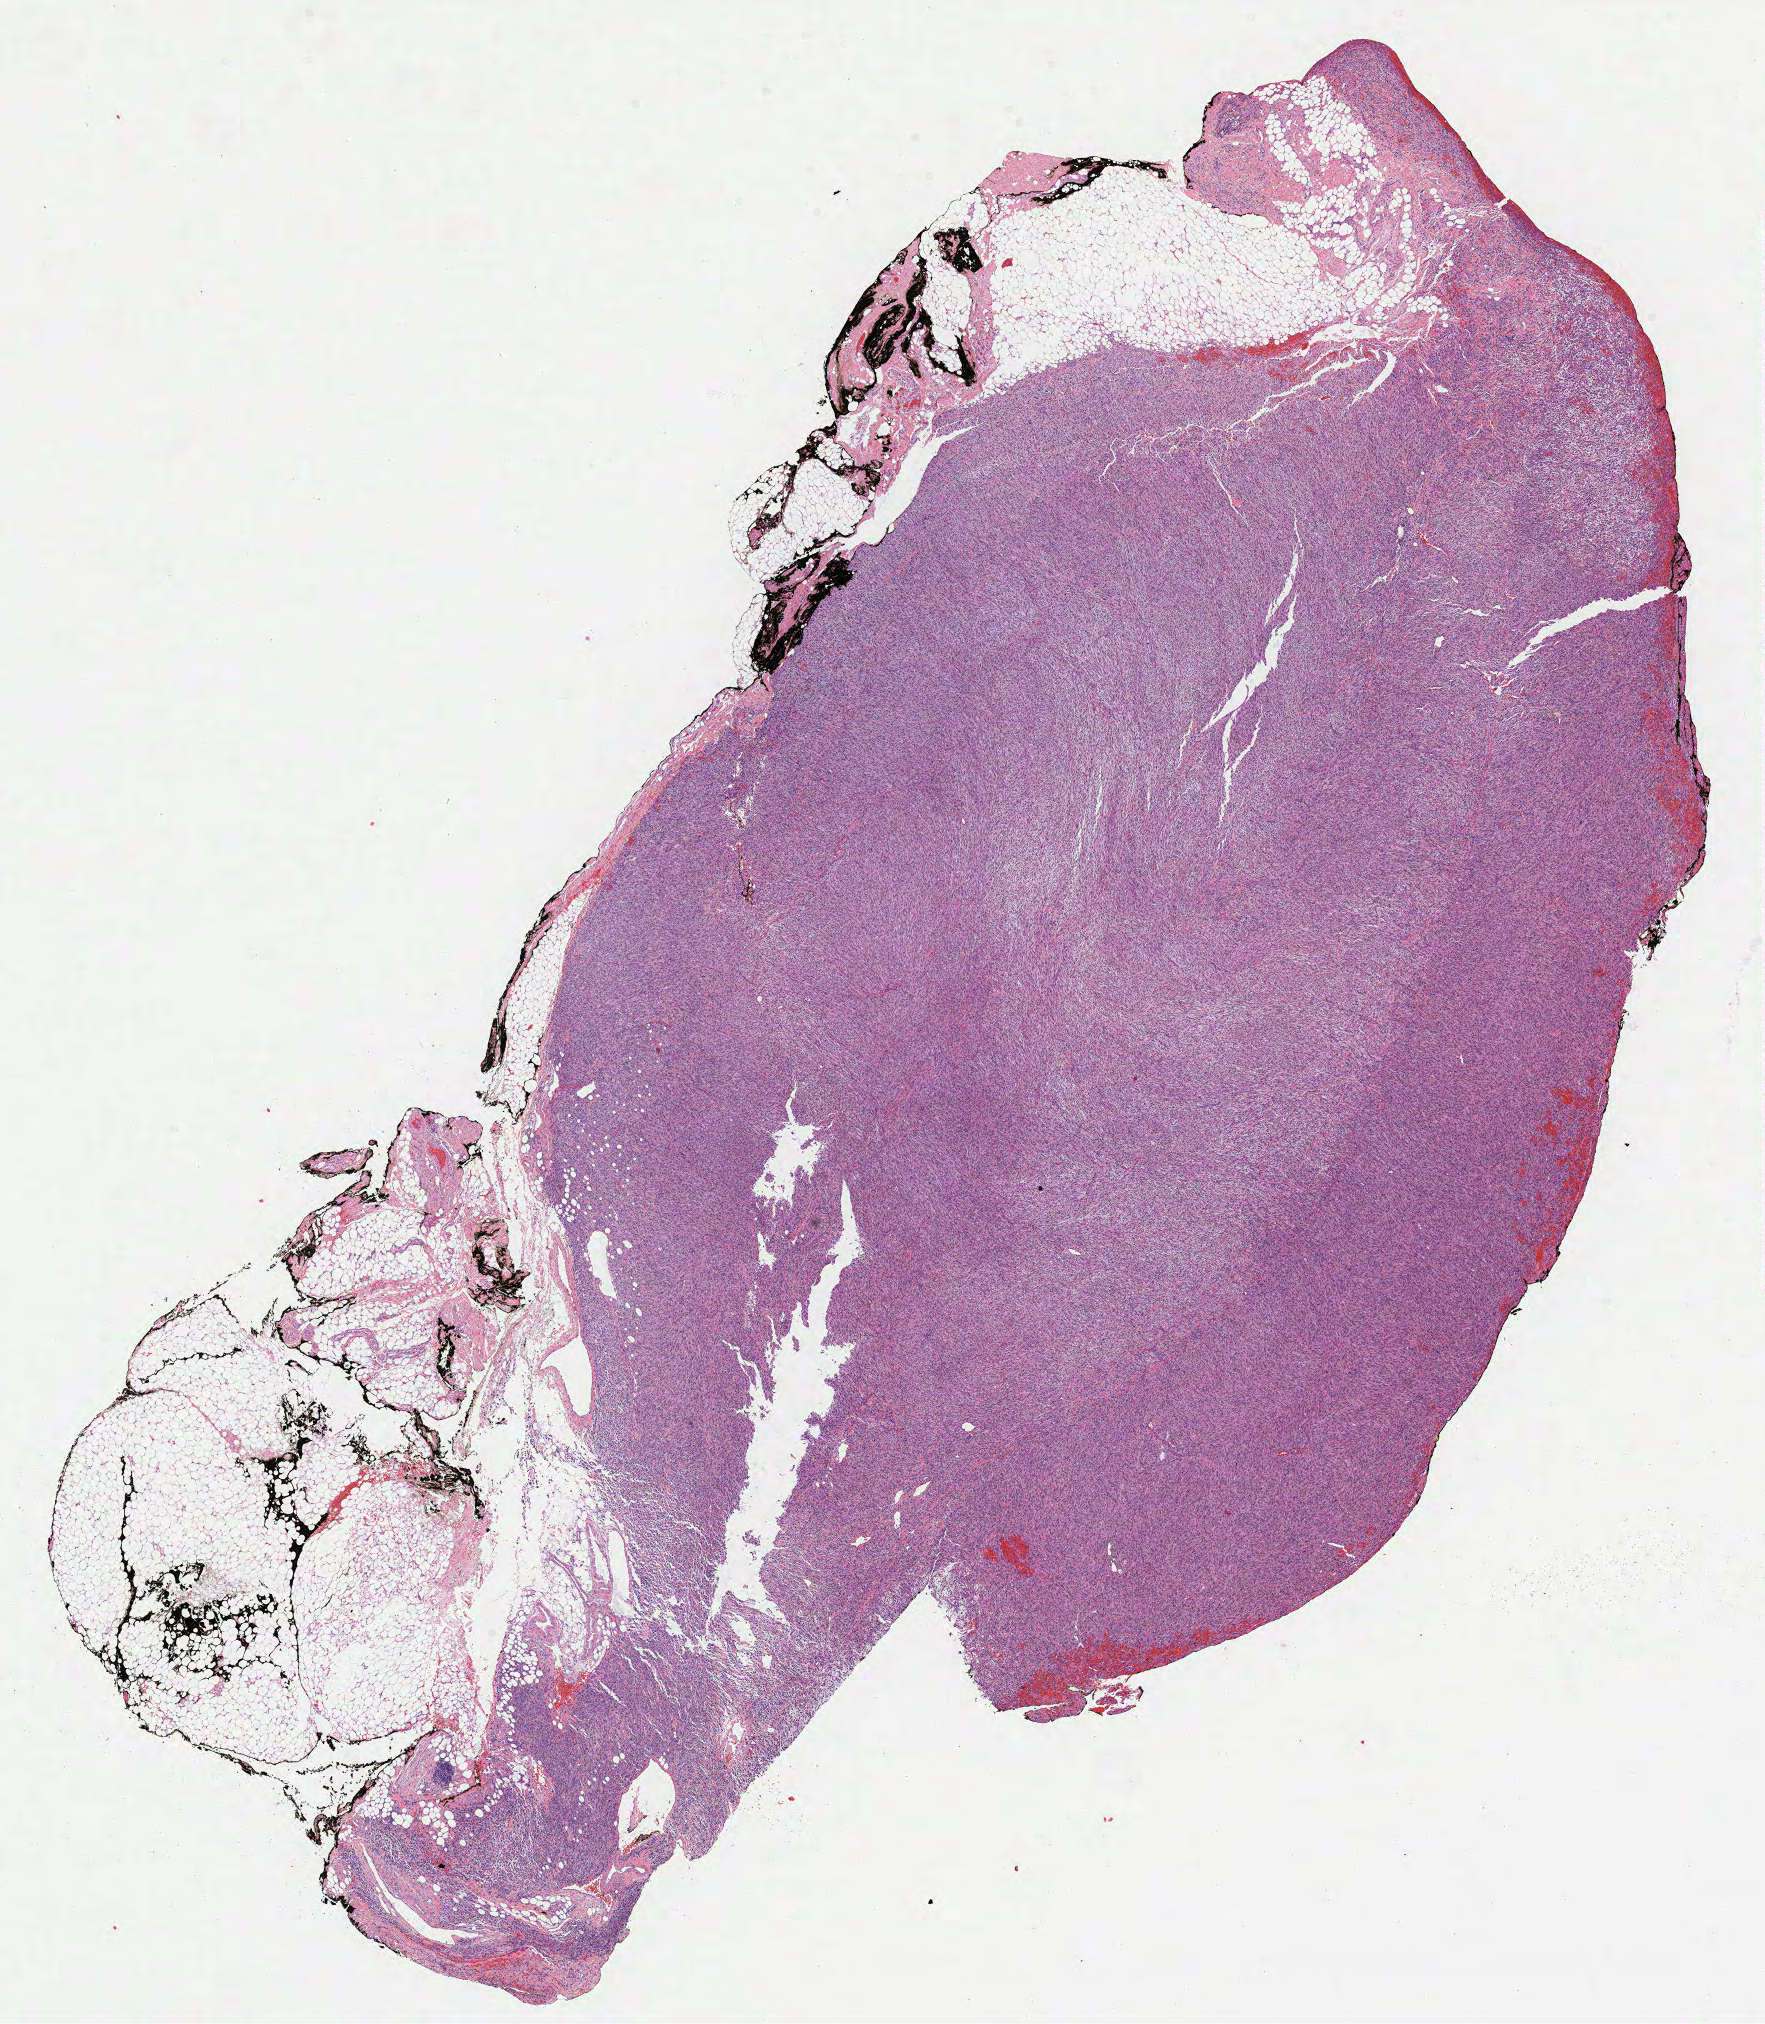
Digitized H&E tissue section (whole slide) — a low-resolution overview of the entire scanned area, about 14.4 x 16.5 mm (from a 40x scan); FFPE section; retroperitoneum and peritoneum, primary tumour sample. Patient: male, age at initial diagnosis 66 years.
Pathologic diagnosis: Dedifferentiated liposarcoma (retroperitoneum).